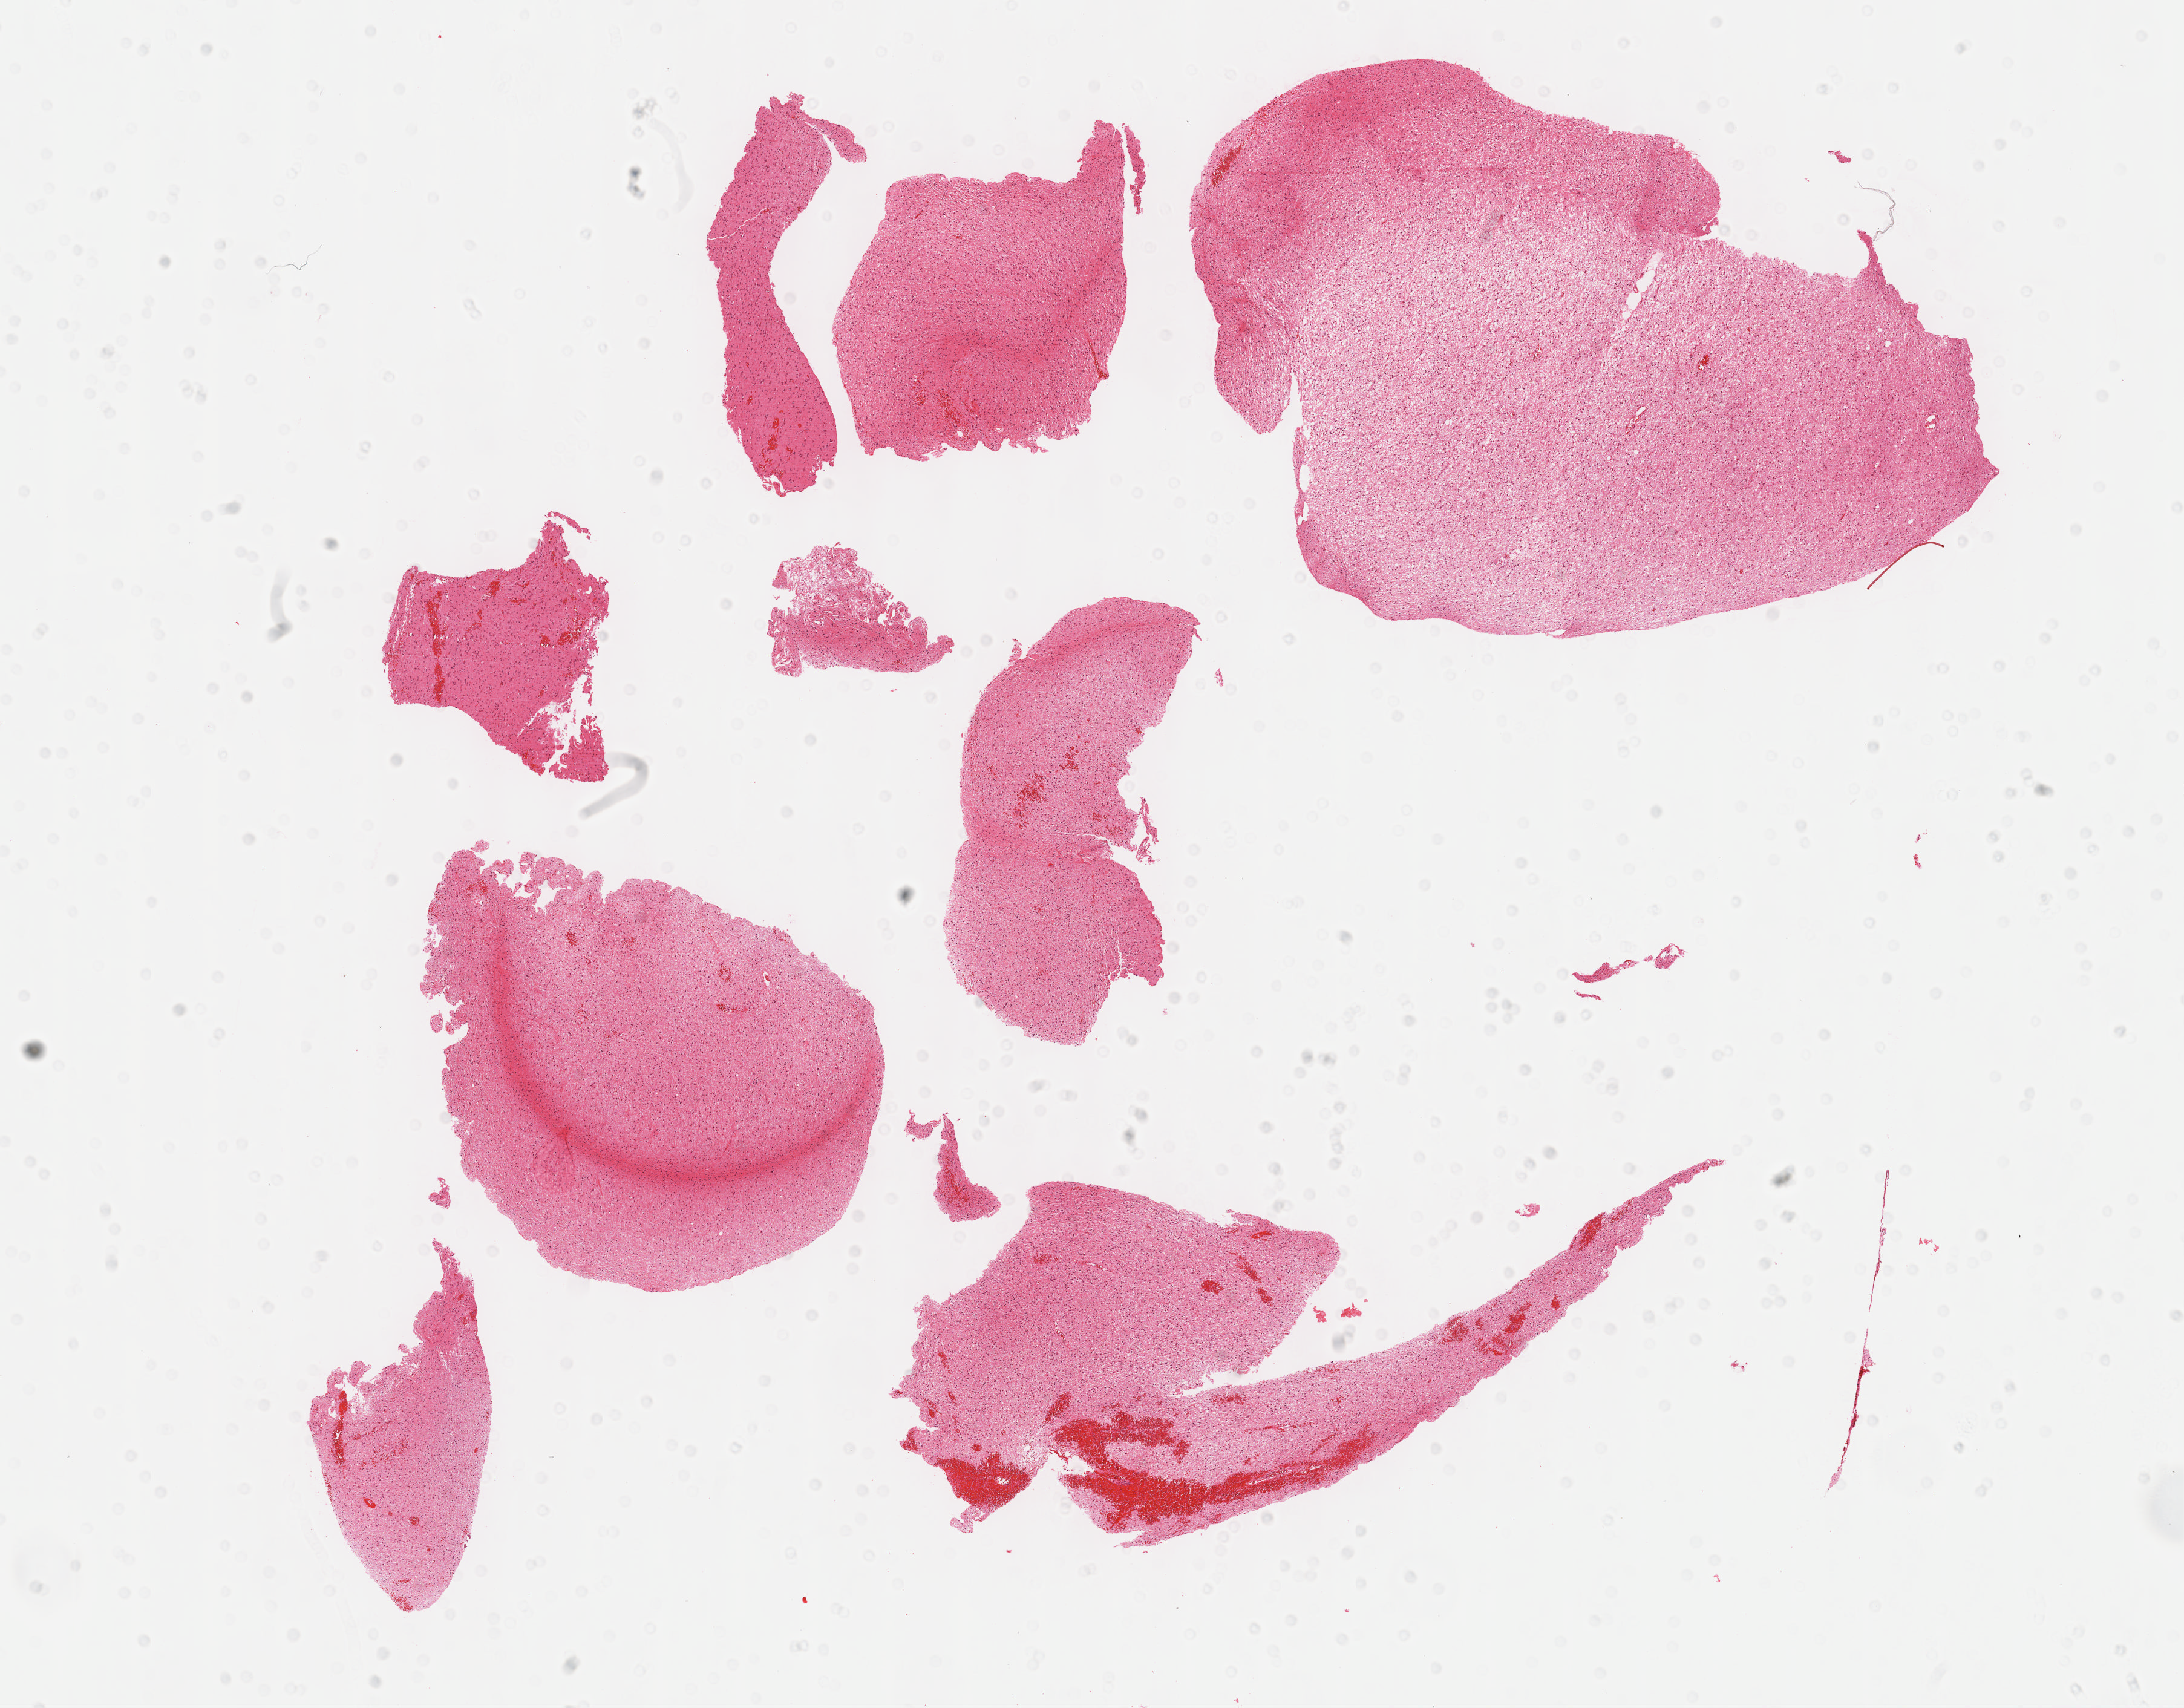
H&E-stained whole-slide image, low-resolution overview of the scanned area, about 14.6 x 11.4 mm (slide scanned at 40x). FFPE section. Sample: primary tumour, brain. Male, age 29 years at initial diagnosis. Histologic grade: G2 (moderately differentiated).
• laterality: left
• pathologic diagnosis: Astrocytoma, NOS (cerebrum)